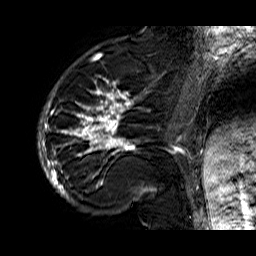
Breast MRI (dynamic contrast-enhanced), one sagittal slice; dynamic contrast-enhanced series, time point 2 of 6 at this slice position (early post-contrast); 1.5 T; TE 6.3 ms, TR 32.9 ms; 256 × 256 image matrix, field of view 200 × 200 mm. Female patient. Case-level facts recorded for this patient, not image findings: setting: breast cancer imaged before/during neoadjuvant chemotherapy; receptor status: HR-positive, HER2-negative.
Annotated regions visible in this slice (semi-automatic segmentation, software-assisted and operator-edited):
- analysis volume of interest (the breast-tissue region the enhancement analysis was run in; not a lesion): bounding box (x1, y1, x2, y2) in pixels: (38, 74, 176, 210)
- tumour enhancement mask (voxels above the 100 % enhancement threshold inside the analysis volume of interest): (38, 74, 176, 202)